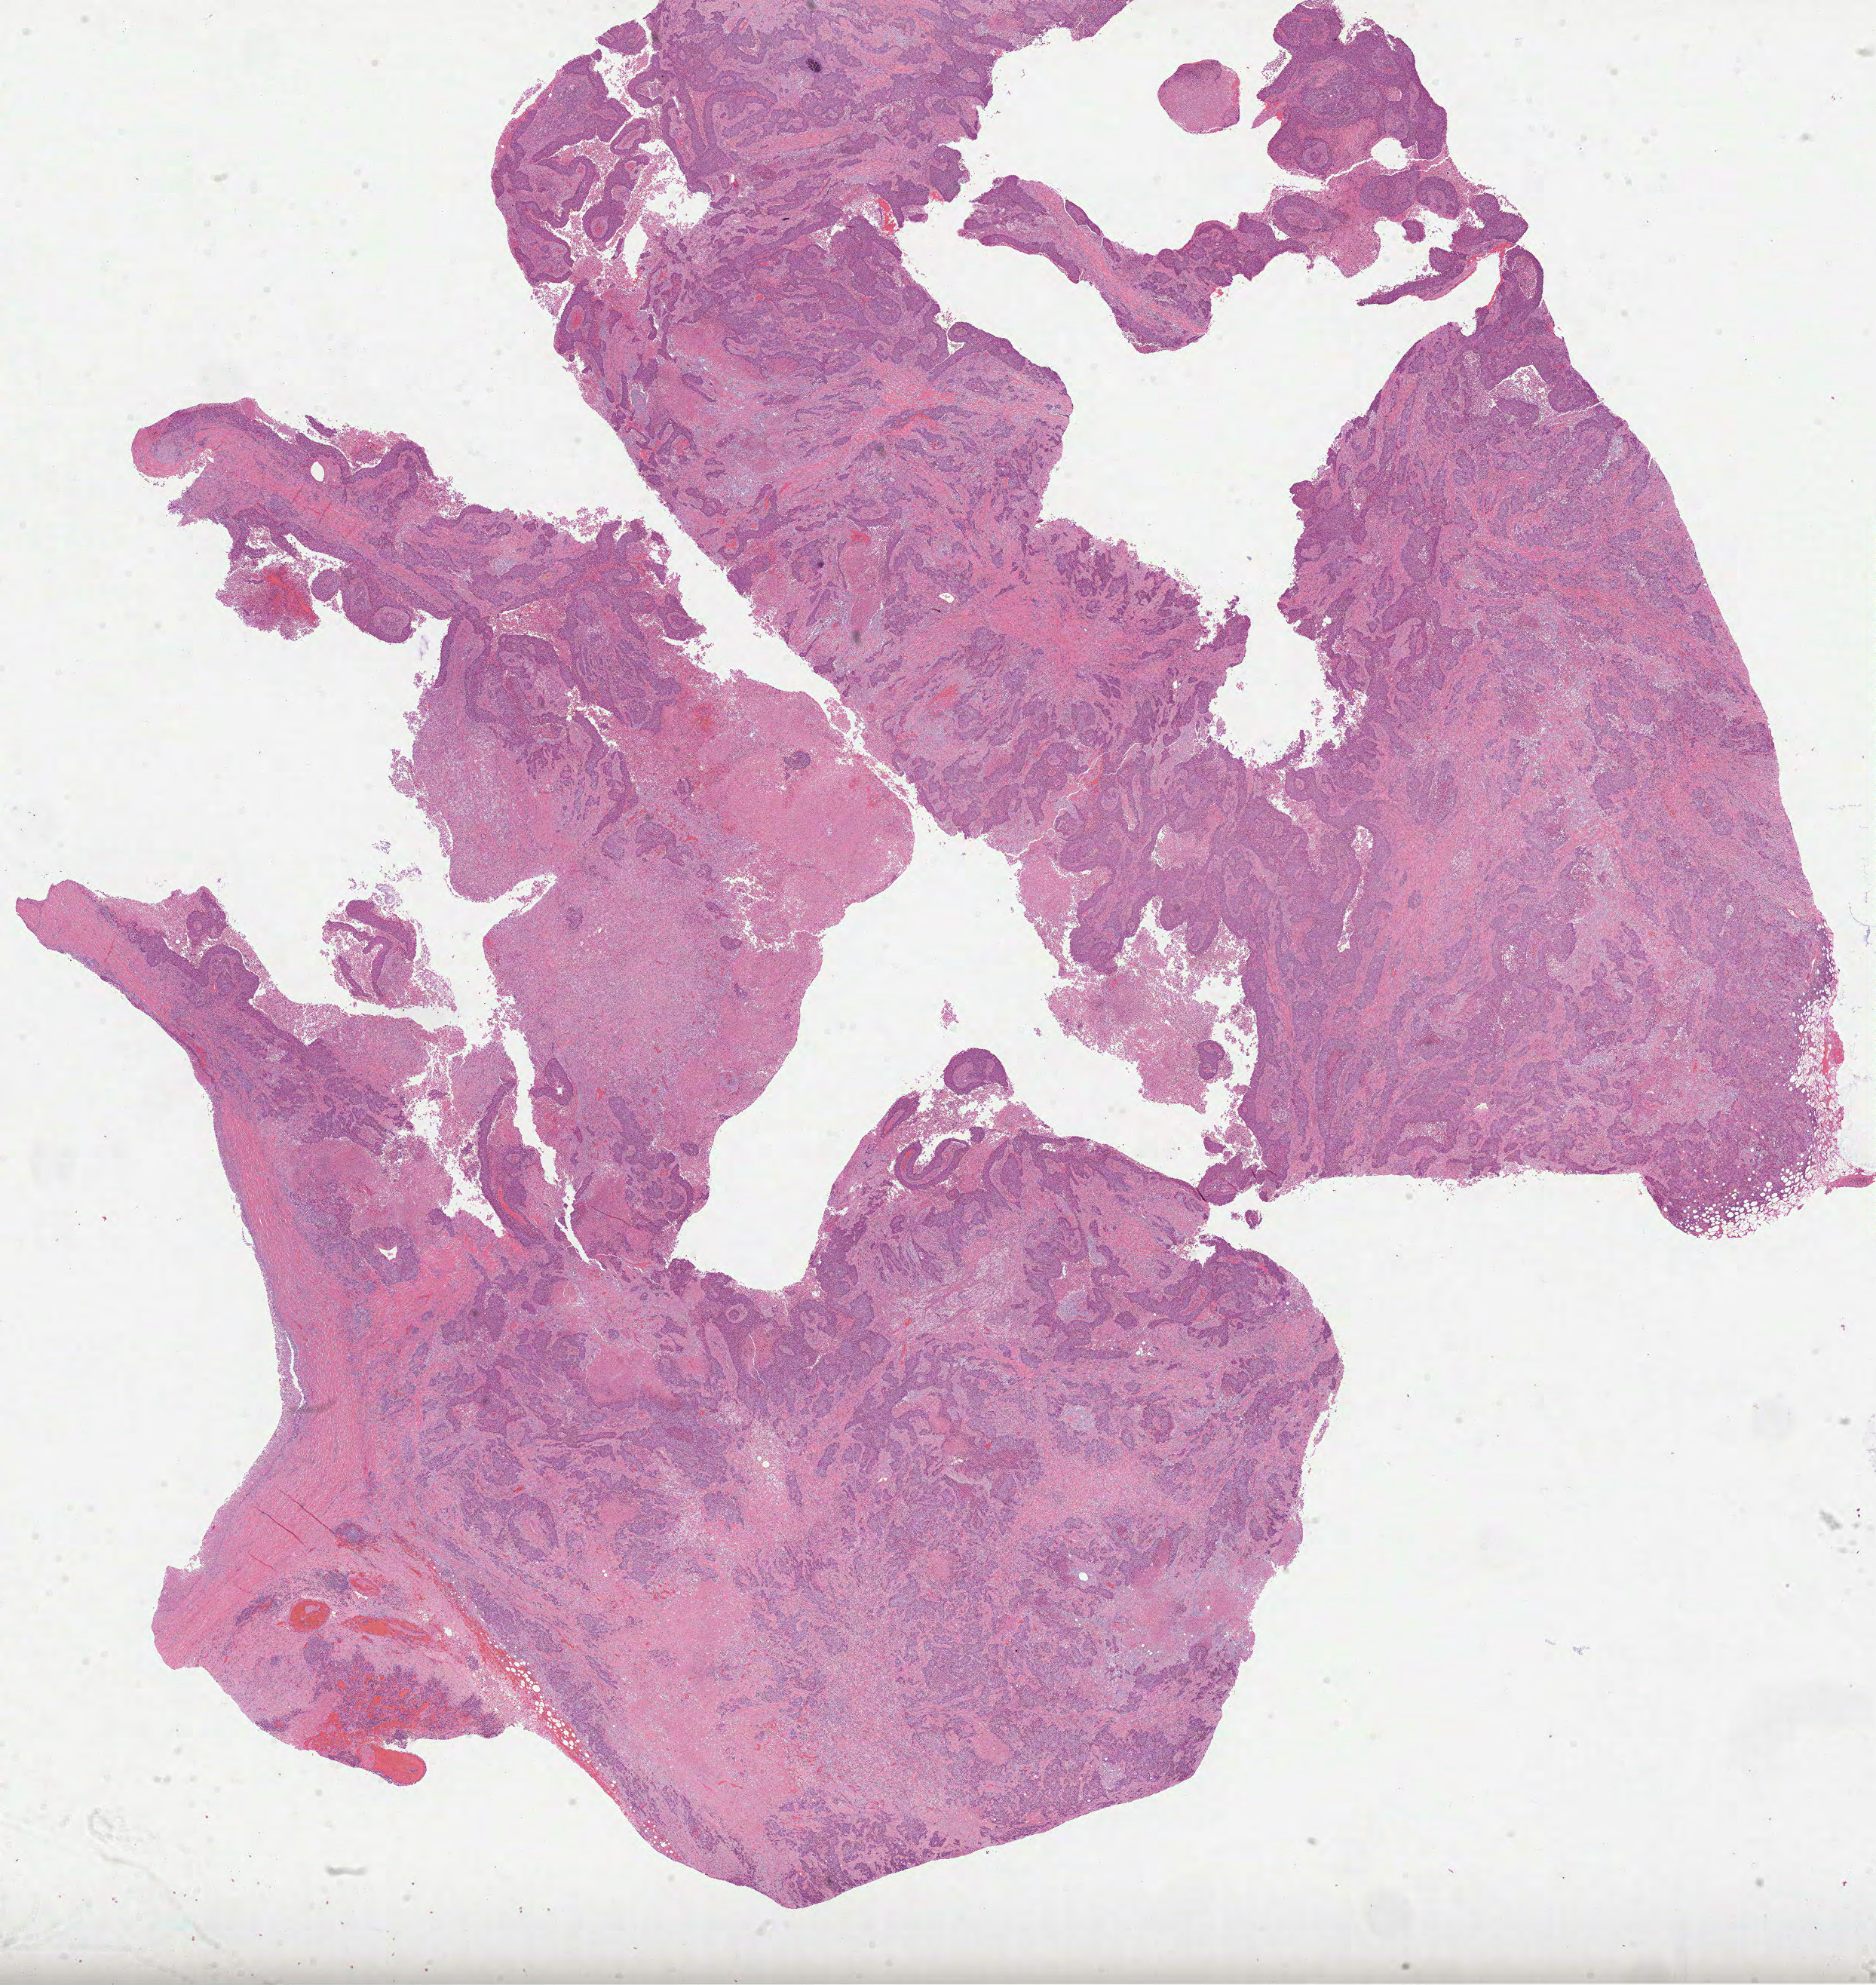
Whole-slide histology image, H&E-stained — a low-resolution overview of the entire scanned area, about 20.1 x 21.2 mm (from a 40x scan). Formalin-fixed paraffin-embedded (FFPE) diagnostic section. Primary tumour sample from the lung. Male patient; age at initial diagnosis 66 years.
- AJCC pathologic stage: IIIA (7th edition)
- laterality: right
- histologic diagnosis: Squamous cell carcinoma, NOS (overlapping lesion of lung)